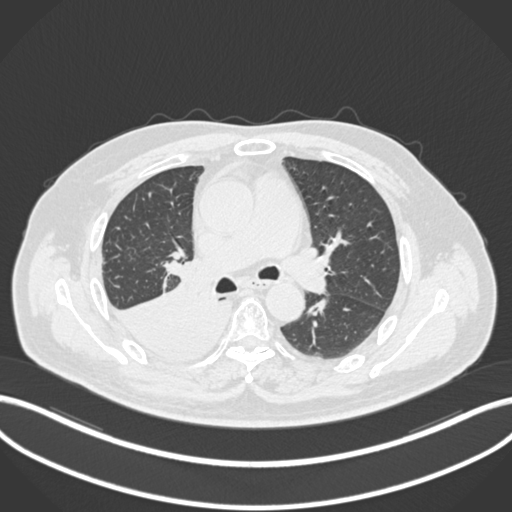
Chest CT, one axial slice; 120 kVp; lung window (W 1500 / L -600 HU); 1 mm slice thickness; 512 × 512 image matrix, field of view 400 × 400 mm. Male patient, age 68 years. Case-level facts recorded for this patient, not image findings: clinical TNM (as recorded): T2a N0 M0.
Structures marked on this image (bounding box drawn by a radiologist):
- lung tumour (recorded histology: adenocarcinoma): bounding box [x1, y1, x2, y2] px = [108, 278, 229, 364]